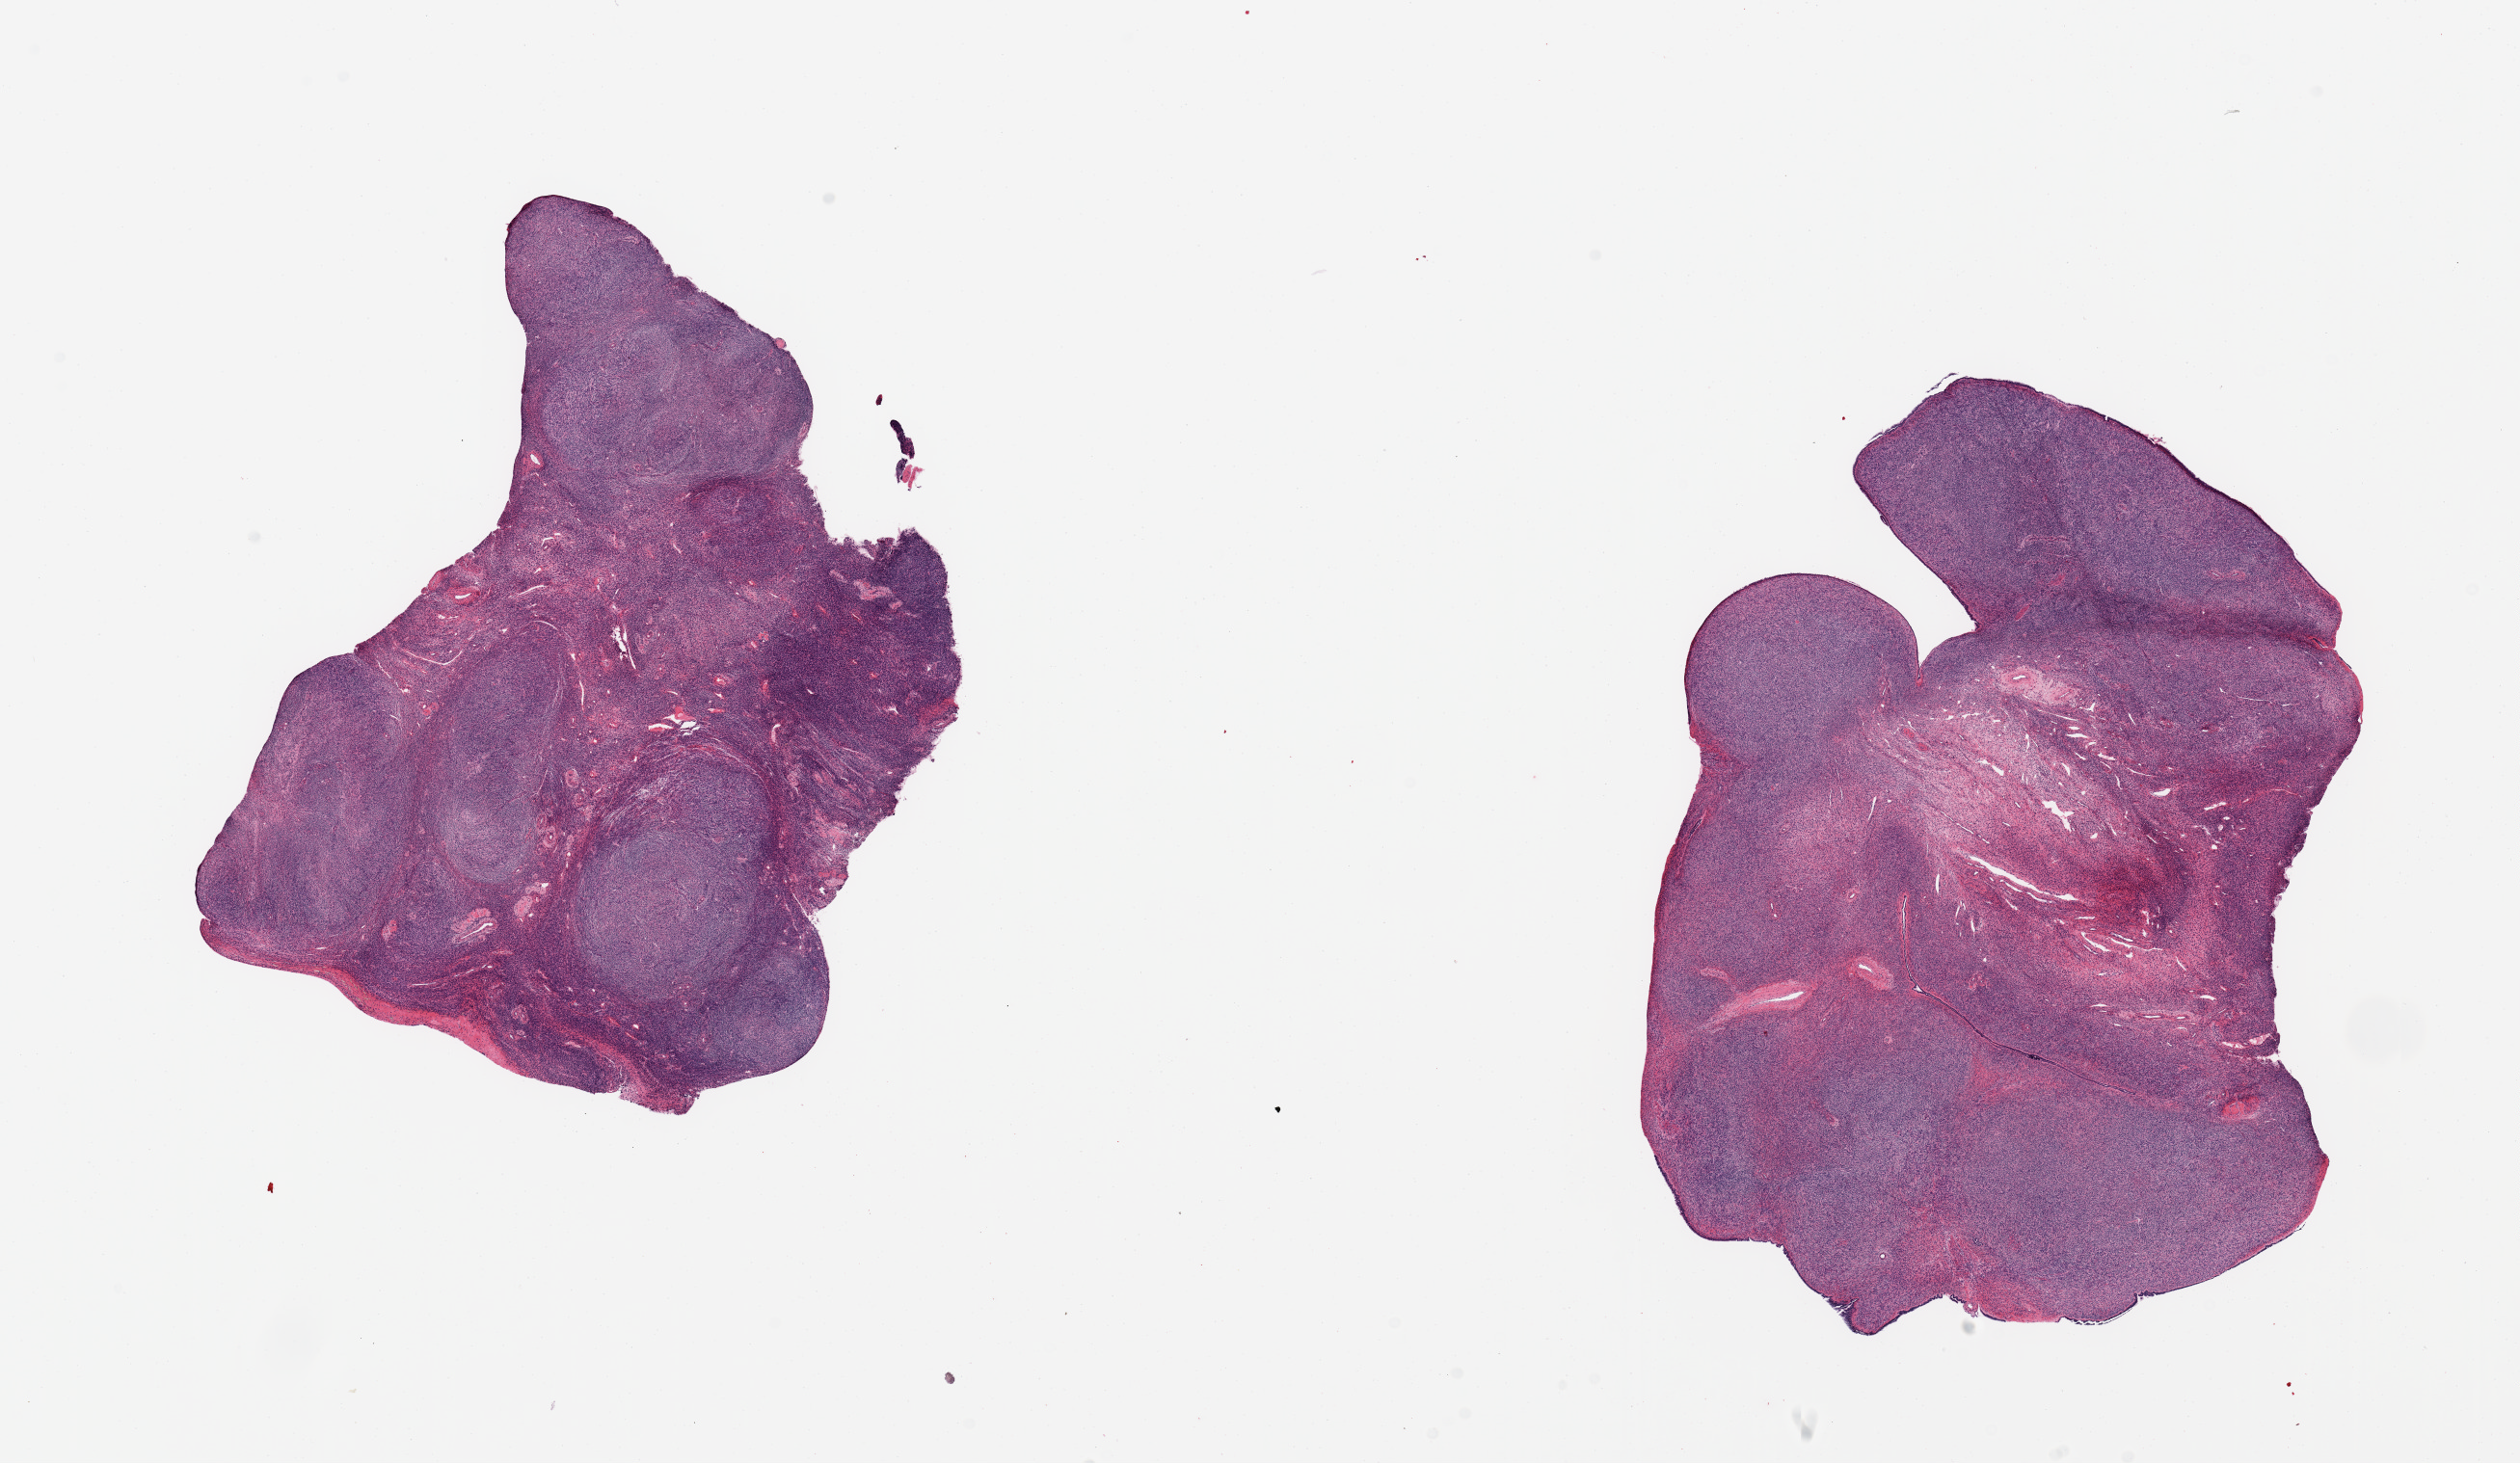
Digitized haematoxylin and eosin-stained section, brightfield, whole scanned area (about 20.7 x 12.0 mm) shown as a low-resolution overview; PAXgene-fixed, paraffin-embedded tissue; section of ovary (target tissue); donor tissue sample. Female donor.
Review note (as recorded): 2 pieces, post menopausal atrophy, normal stroma.